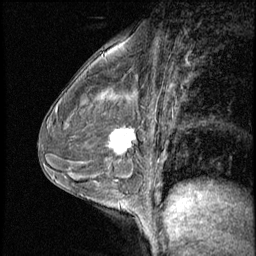
Breast MRI (dynamic contrast-enhanced), one sagittal slice. Slice 37 of 56 in the series (ordered by position). 3 images stored at this slice position (order not interpretable as contrast timing). 1.5 T. TE 4.2 ms, TR 8.7 ms. 2.5 mm slice thickness. 256 × 256 image matrix, field of view 180 × 180 mm. Female patient, age 43 years. From the clinical record (not read from this slice): setting: breast cancer imaged before/during neoadjuvant chemotherapy; receptor status: HR-positive, HER2-negative.
Structures marked on this image (semi-automatic segmentation, software-assisted and operator-edited):
- analysis volume of interest (the breast-tissue region the enhancement analysis was run in; not a lesion): bounding box (x1, y1, x2, y2) in pixels: (101, 120, 145, 165)
- tumour enhancement mask (voxels above the 140 % enhancement threshold inside the analysis volume of interest): (111, 128, 136, 153)